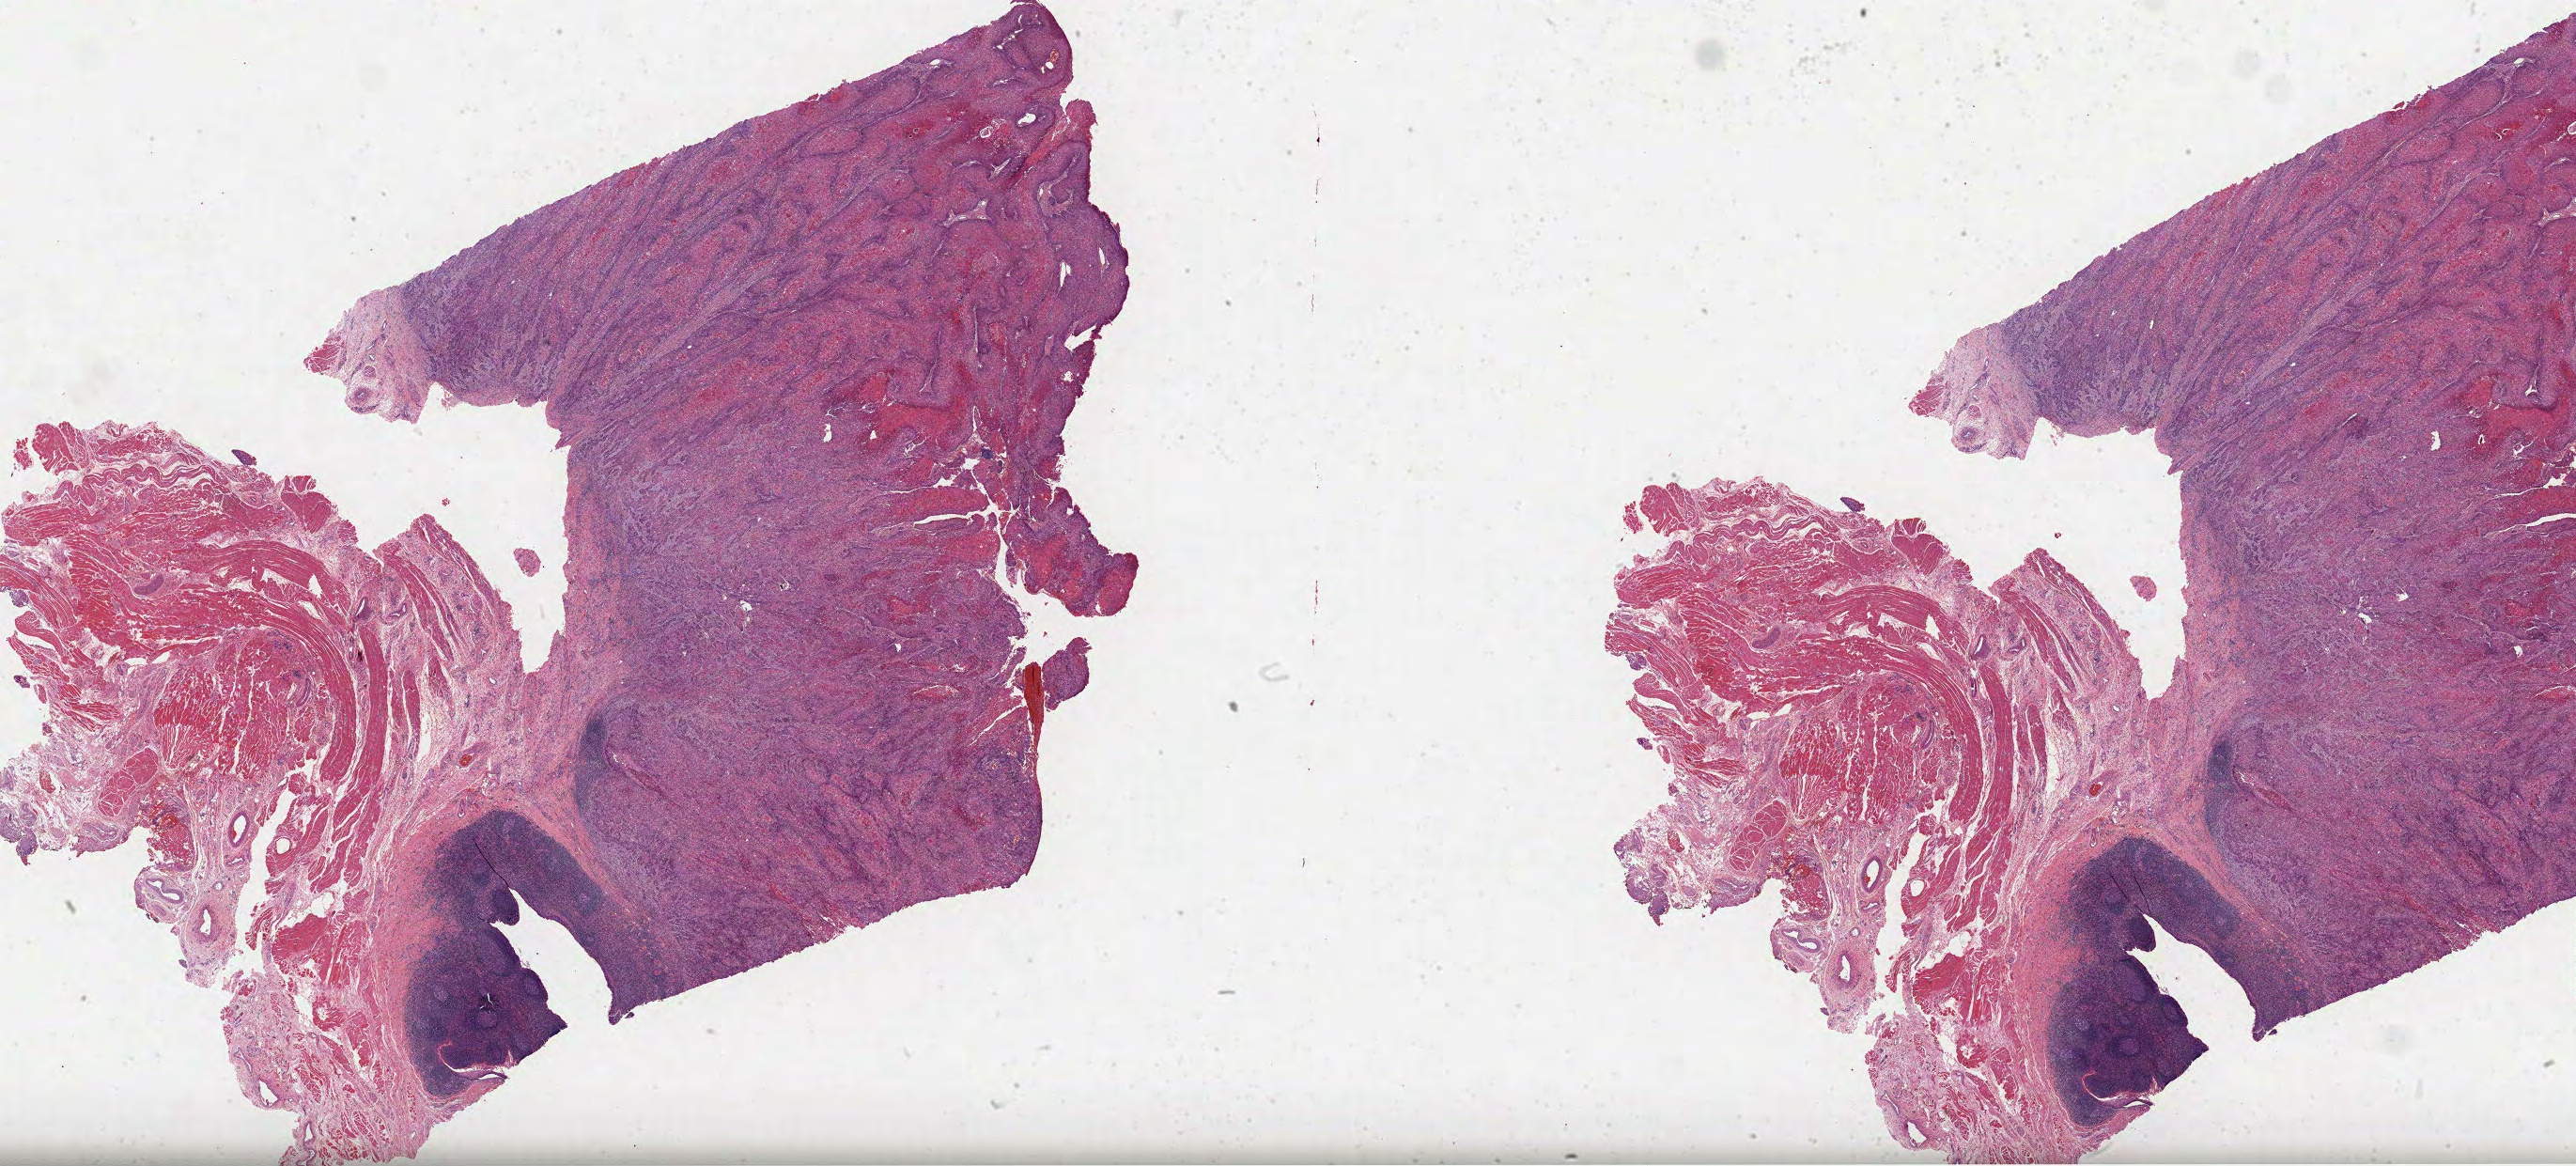
Hematoxylin and eosin (H&E) stained whole-slide image — a low-resolution overview of the entire scanned area, about 44.2 x 20.0 mm. Formalin-fixed paraffin-embedded (FFPE) diagnostic section. Head and neck, primary tumour sample. Male patient; age at initial diagnosis 38 years. Histologic grade: G2 (moderately differentiated).
AJCC pathologic stage: IVB (6th edition). Lymph nodes positive (case pathology): 1 of 9 examined. Diagnosis: Squamous cell carcinoma, NOS (tonsil, NOS). TNM: T2 N3.